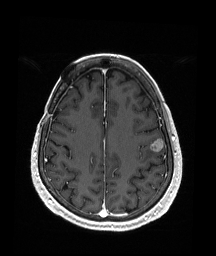
Brain MRI from a brain-tumour surgery series, one axial slice; position 64 of 176 along the scan axis; T1-weighted post-contrast; 216 × 256 image matrix, field of view 211 × 250 mm. From the clinical record (not read from this slice): histopathology: Metastatic Malignant Melanoma.
Annotated regions visible in this slice (expert manual segmentation):
- tumour: box from (x=150, y=139) to (x=164, y=153) px